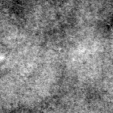
Crop from a digitized film mammogram around one marked abnormality, right breast, CC view.
Marked abnormality: calcifications, morphology pleomorphic, distribution clustered; BI-RADS assessment category 4; pathology result (as recorded, not read from the image): malignant.